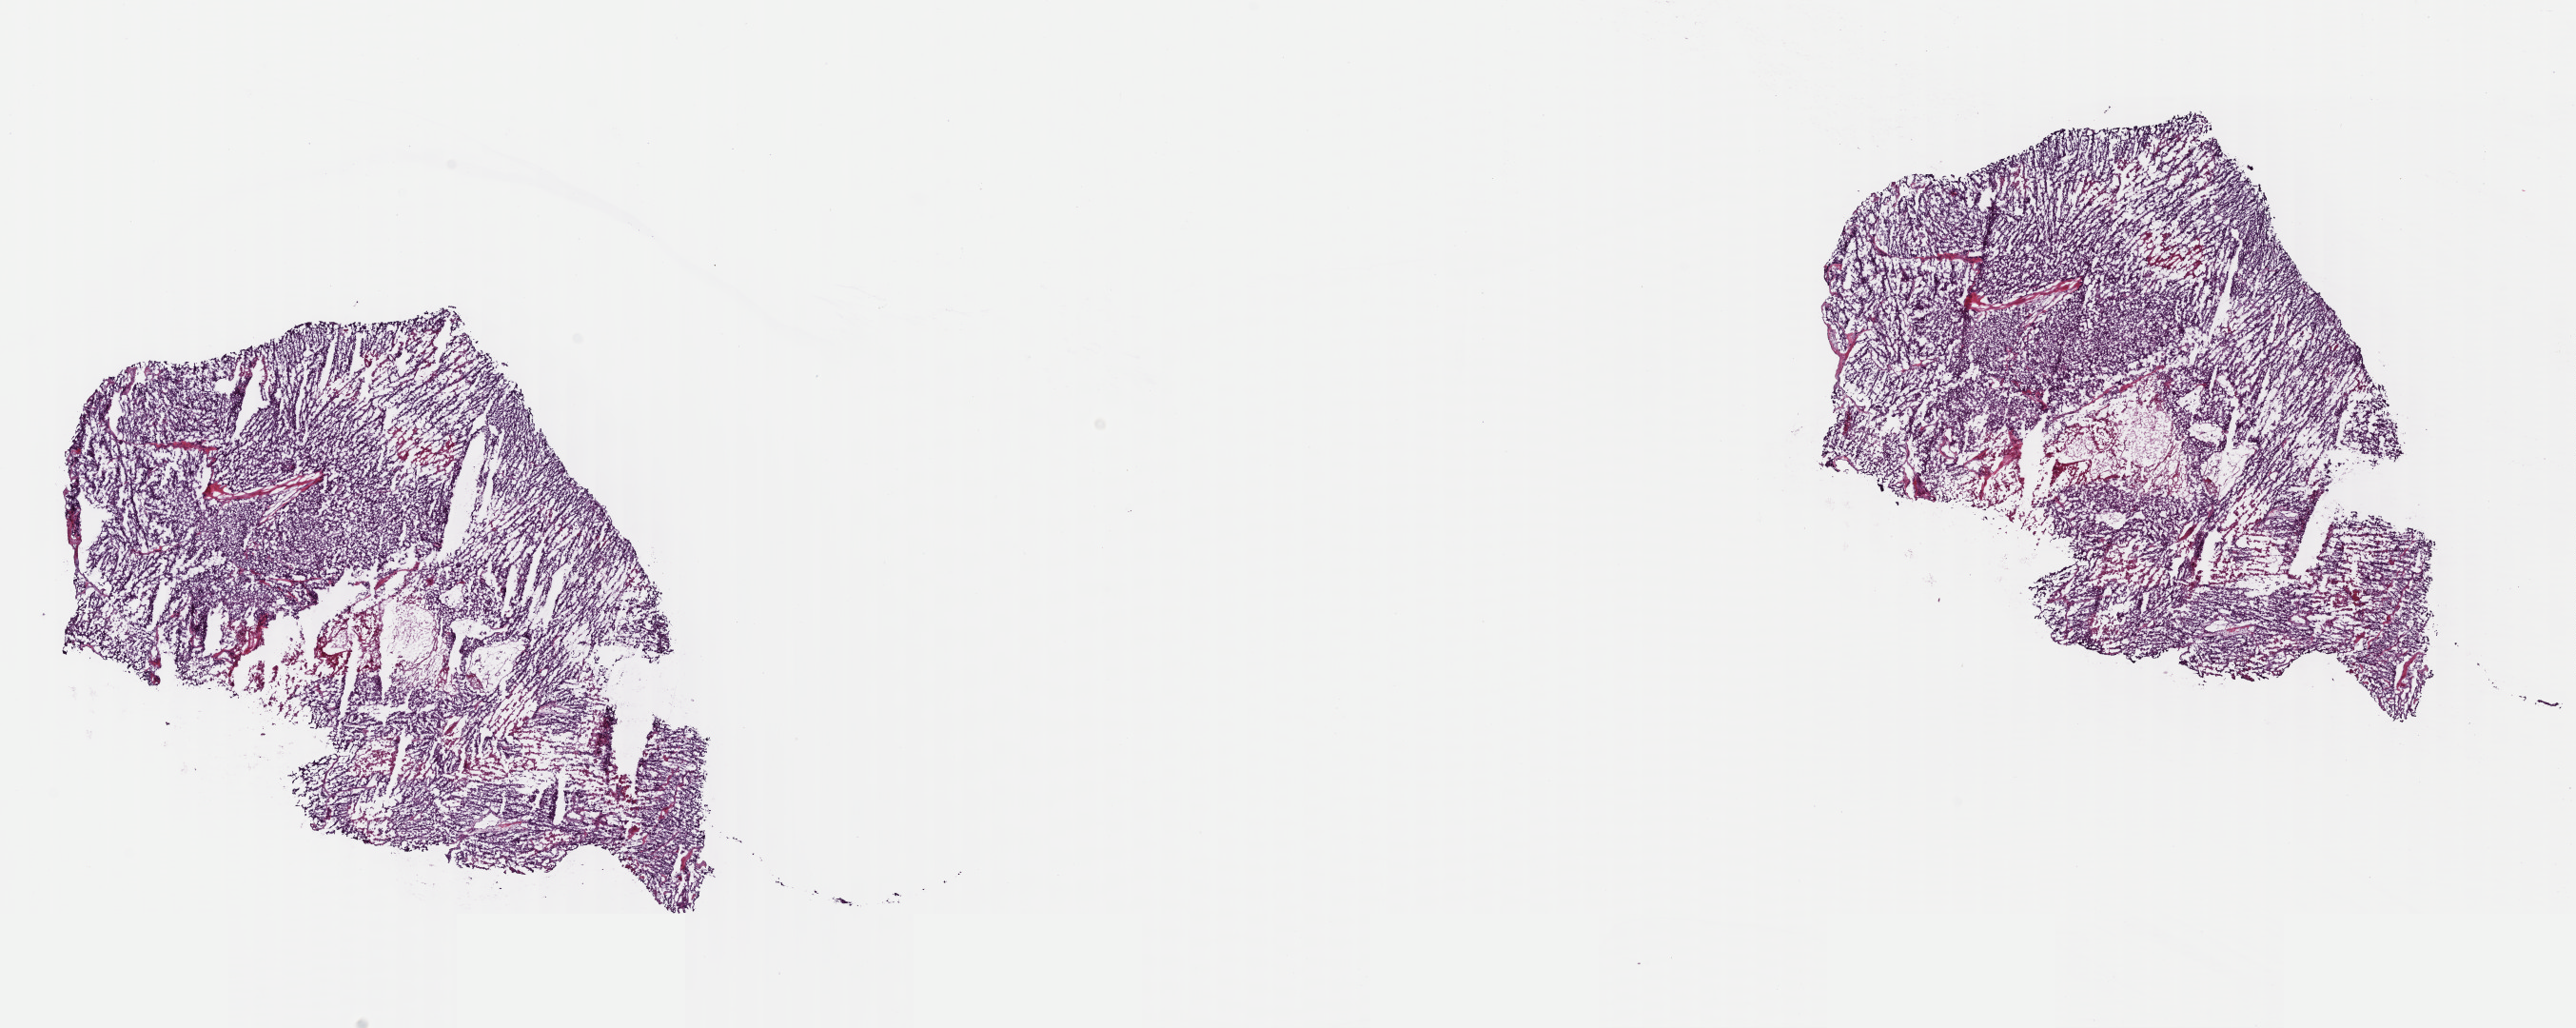
Whole-slide histology image, Hematoxylin and eosin (H&E) stained, low-resolution overview of the scanned area, about 21.3 x 8.5 mm. Frozen section. Primary tumour sample from the adrenal cortex. Female, age 69 years at initial diagnosis. Pathologist review of this section (percent, as recorded): tumour cells 70%, tumour nuclei 100%, normal cells 0%, stromal cells 10%, necrosis 20%. Infiltration values recorded for this section: lymphocyte infiltration 0%, monocyte infiltration 0%, neutrophil infiltration 0%.
- pathologic diagnosis: Adrenal cortical carcinoma
- laterality: left